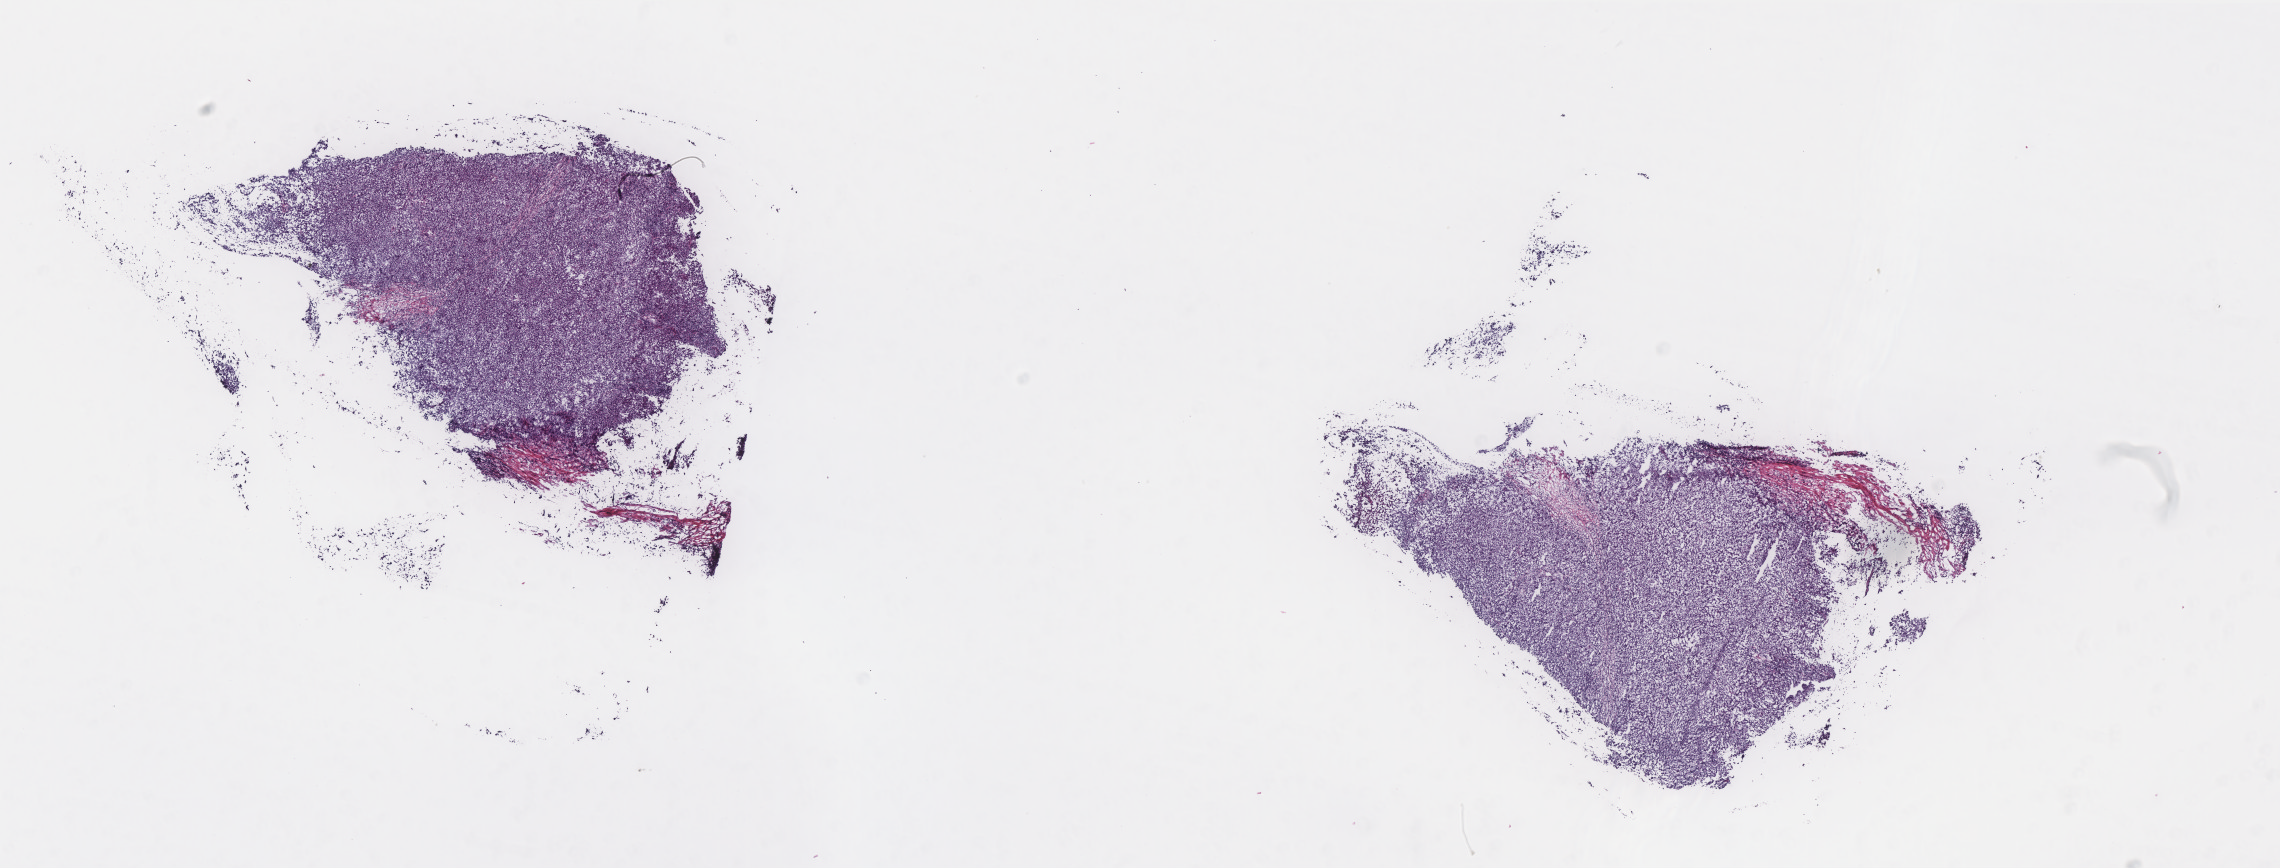
Whole-slide histology image, Hematoxylin and eosin (H&E) stained, a low-resolution overview of the entire scanned area, about 18.3 x 7.0 mm (acquisition: 40x scan). Frozen section from the top of the tissue portion. Metastatic tumour sample, sampled site not recorded. Patient: female, age at initial diagnosis 47 years. Composition of this section per pathologist review: tumour cells 90%, tumour nuclei 90%, normal cells 0%, stromal cells 9%, necrosis 1%. Inflammatory infiltration, as recorded: lymphocyte infiltration 1%, monocyte infiltration 0%, neutrophil infiltration 0%.
This section: metastatic tumour tissue. Patient diagnosis: Malignant melanoma, NOS.